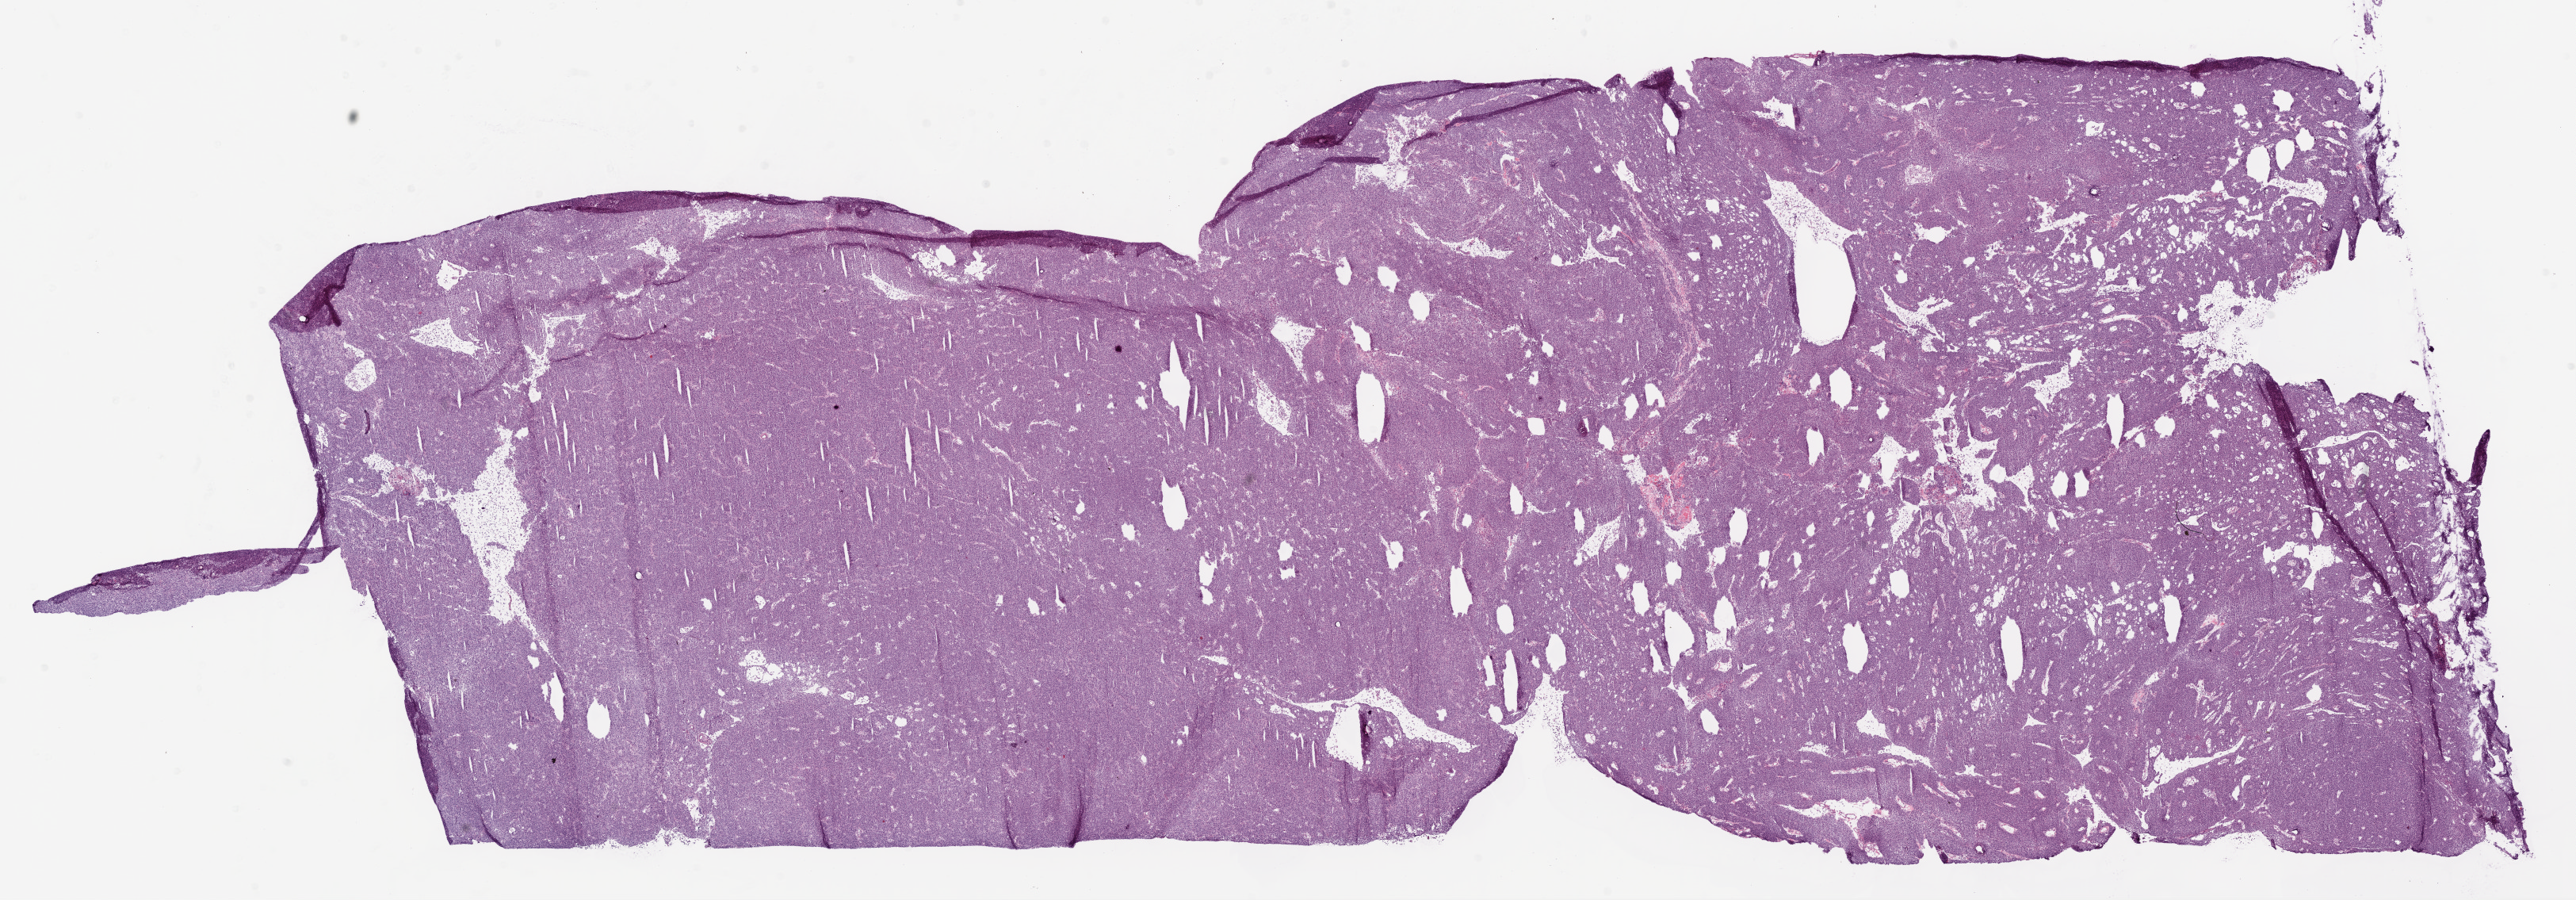
Digitized H&E tissue section (whole slide) — shown as a low-resolution overview of the whole scanned area (about 26.1 x 9.1 mm, from a 20x scan). Frozen section from the bottom of the tissue portion. Sample: primary tumour, ovary. Patient: female, age at initial diagnosis 61 years. Histologic grade: G3 (poorly differentiated). Composition of this section per pathologist review: tumour cells 92%, tumour nuclei 90%, normal cells 0%, stromal cells 5%, necrosis 3%.
FIGO stage: IIIC. Pathologic diagnosis: Serous cystadenocarcinoma, NOS.